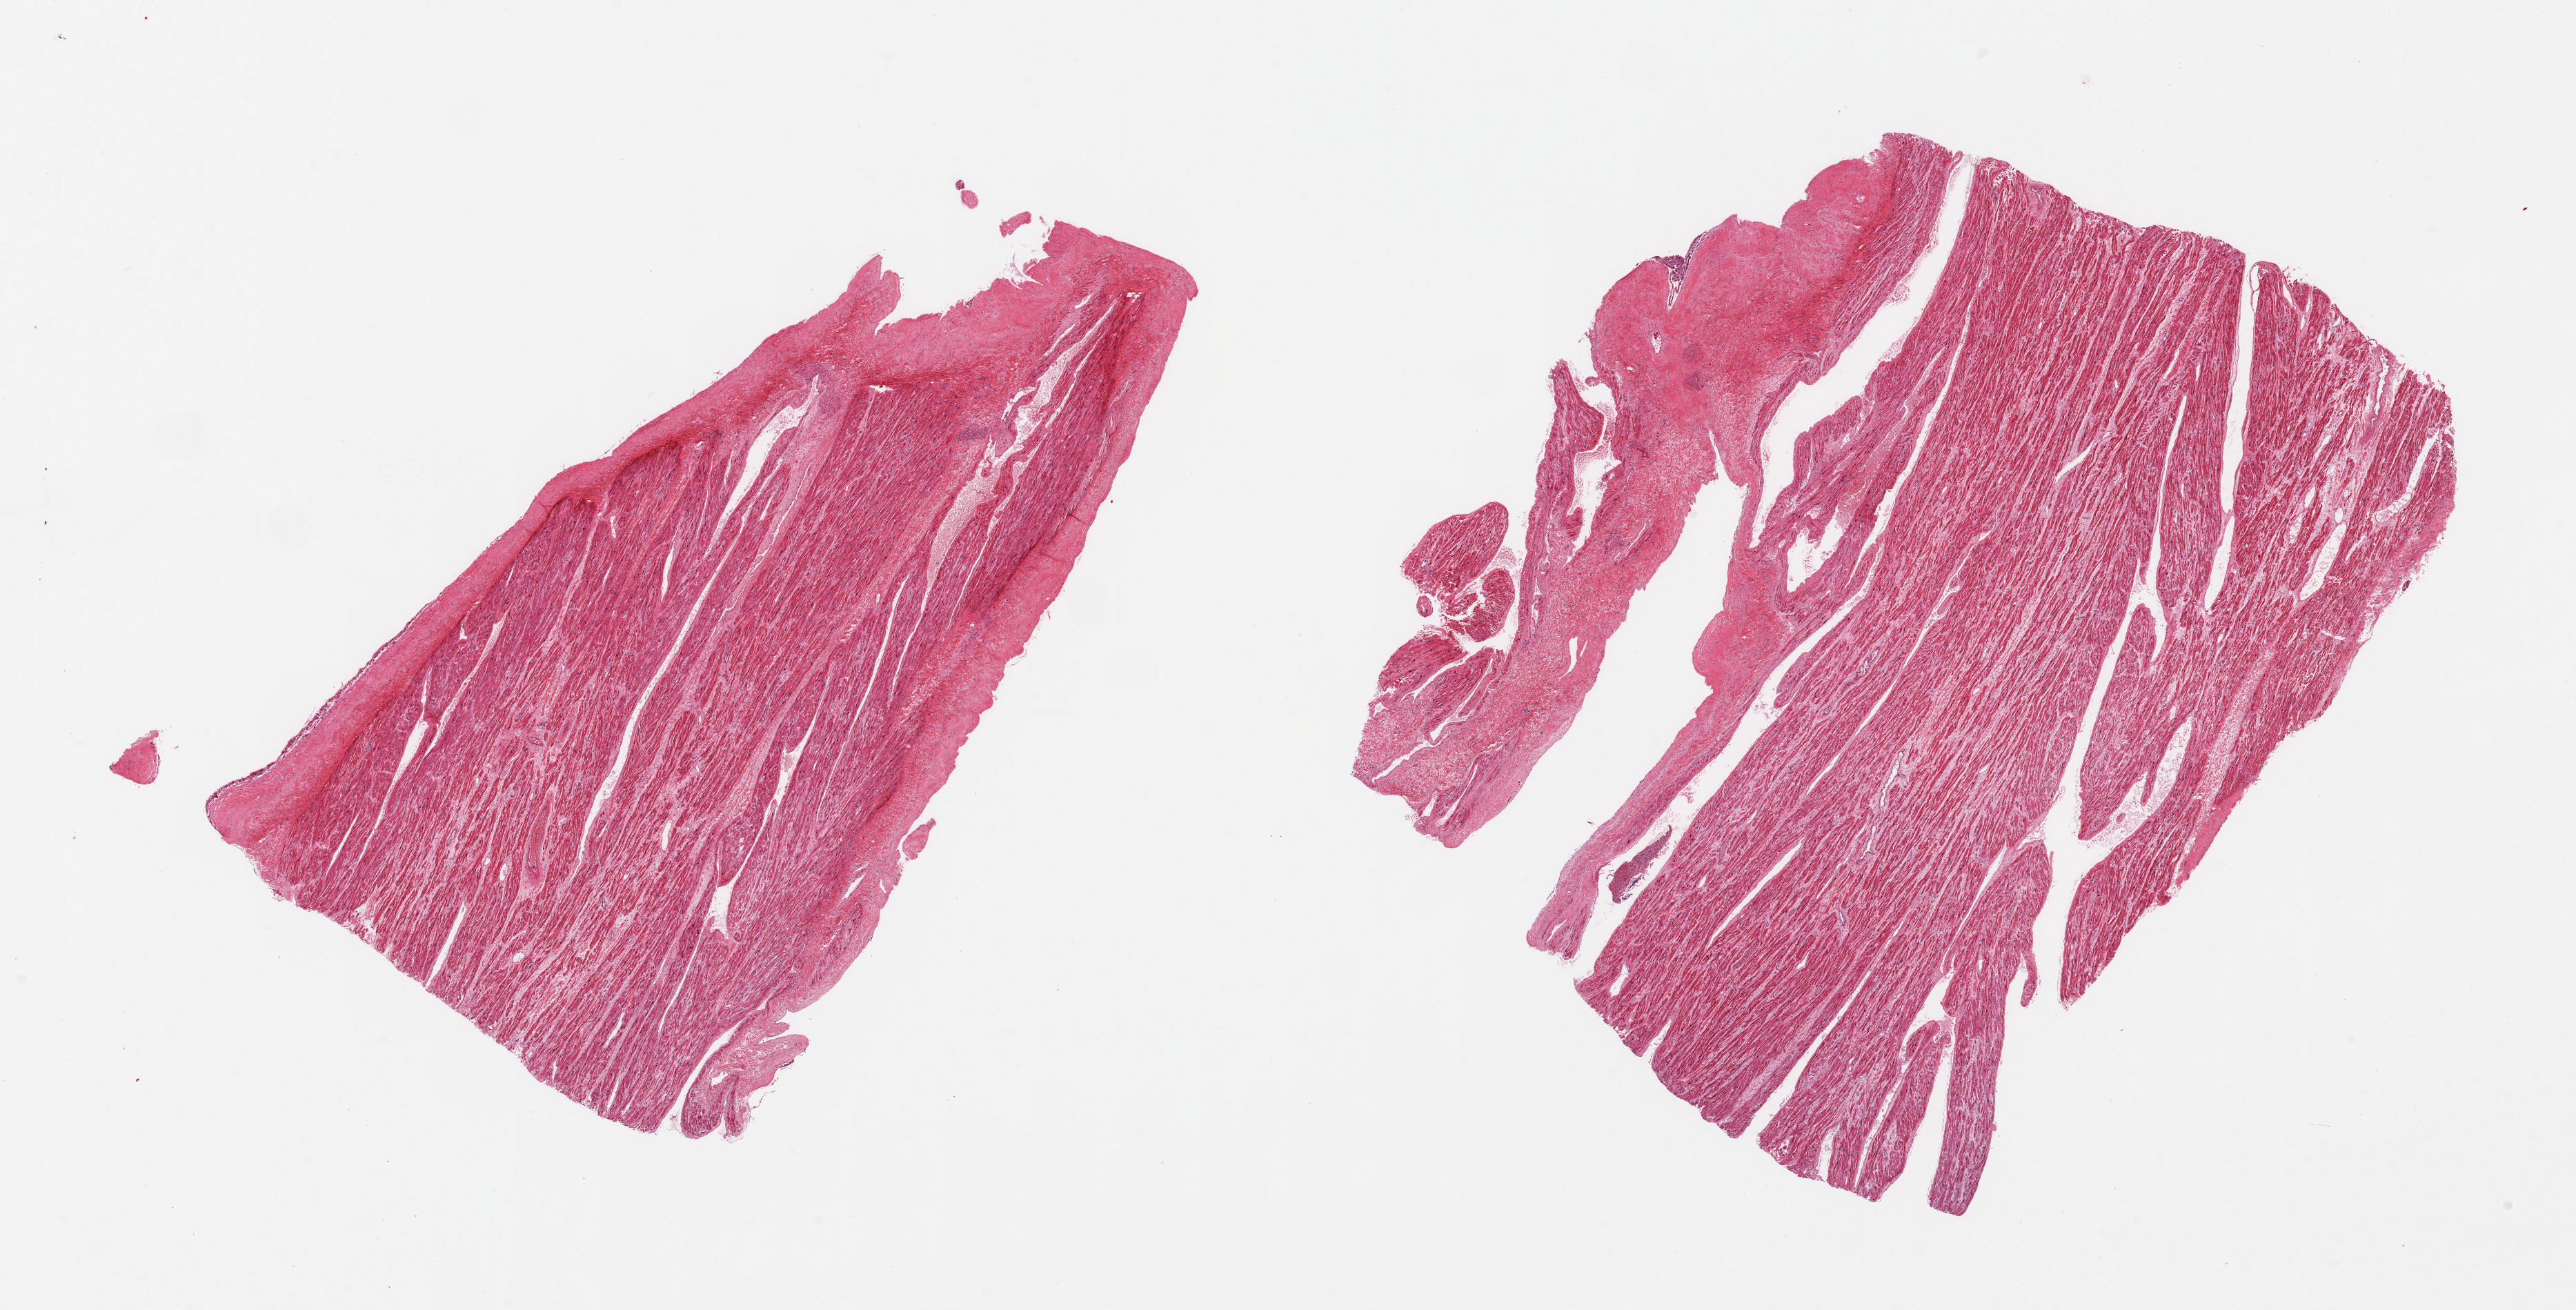
Hematoxylin and eosin (H&E) whole-slide image, brightfield — a low-resolution overview of the entire scanned area, about 29.5 x 15.0 mm (from a 20x scan); PAXgene-fixed, paraffin-embedded tissue; sampled site (target tissue): auricular appendage; donor tissue sample. Male donor.
Reviewer comment on this tissue sample: 2 pieces, no abnormalities.